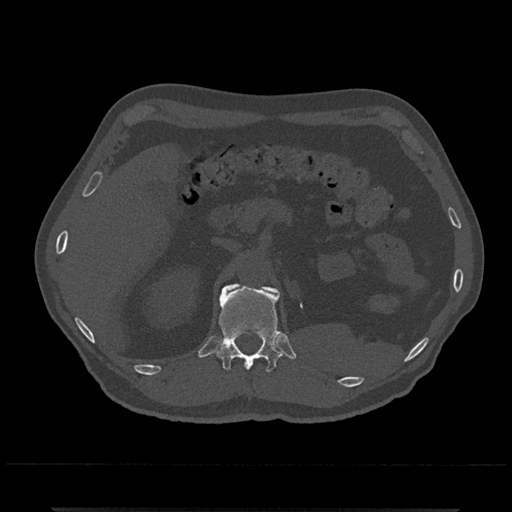
CT including the spine, one axial slice; position 427 of 797 along the scan axis; reconstruction kernel Br40s/3; bone window (W 1800 / L 400 HU); 0.5 mm slice thickness; 512 × 512 image matrix, field of view 393 × 393 mm. Male patient, age 67 years. Case-level facts recorded for this patient, not image findings: primary cancer: prostate.
Structures marked on this image (semi-automatically segmented with operator editing):
- L1 vertebra: bounding box <259,284,272,291> (left, top, right, bottom; pixels)
- T12 vertebra: <214,284,282,372>